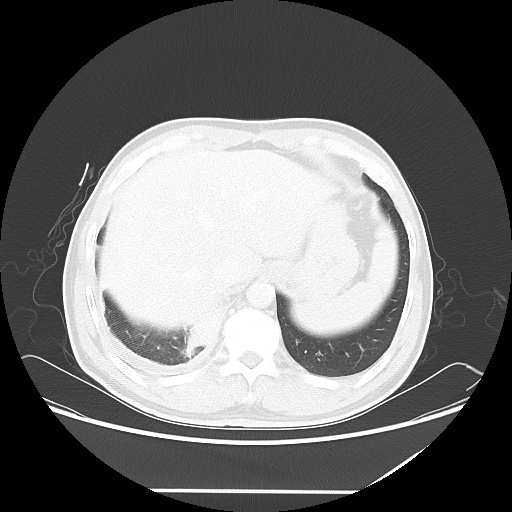
Chest CT, one axial slice. Slice 12 of 60 in the series (ordered by position). Lung window (W 1500 / L -600 HU). 5 mm slice thickness. 512 × 512 image matrix. Male patient, age 48 years. From the clinical record (not read from this slice): clinical TNM (as recorded): T3 N3 M1a.
Annotated regions visible in this slice (bounding box drawn by a radiologist):
- lung tumour (recorded histology: squamous cell carcinoma): bounding box <183,291,227,358> (left, top, right, bottom; pixels)